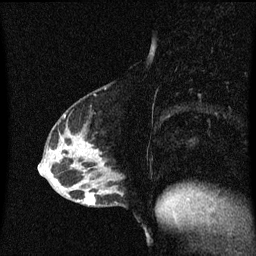
Breast MRI (dynamic contrast-enhanced), one sagittal slice. Position 22 of 60 along the scan axis. Dynamic contrast-enhanced series, image 2 of 3 at this slice position (ordered by acquisition). 1.5 T. TE 4.2 ms, TR 8.4 ms. 2 mm slice thickness. 256 × 256 image matrix, field of view 200 × 200 mm. Female patient, age 40 years.
Structures marked on this image (semi-automatic segmentation, software-assisted and operator-edited):
- analysis volume of interest (the breast-tissue region the enhancement analysis was run in; not a lesion): bounding box <82,172,126,207> (left, top, right, bottom; pixels)
- tumour enhancement mask (voxels above the 70 % enhancement threshold inside the analysis volume of interest): <85,194,96,205>